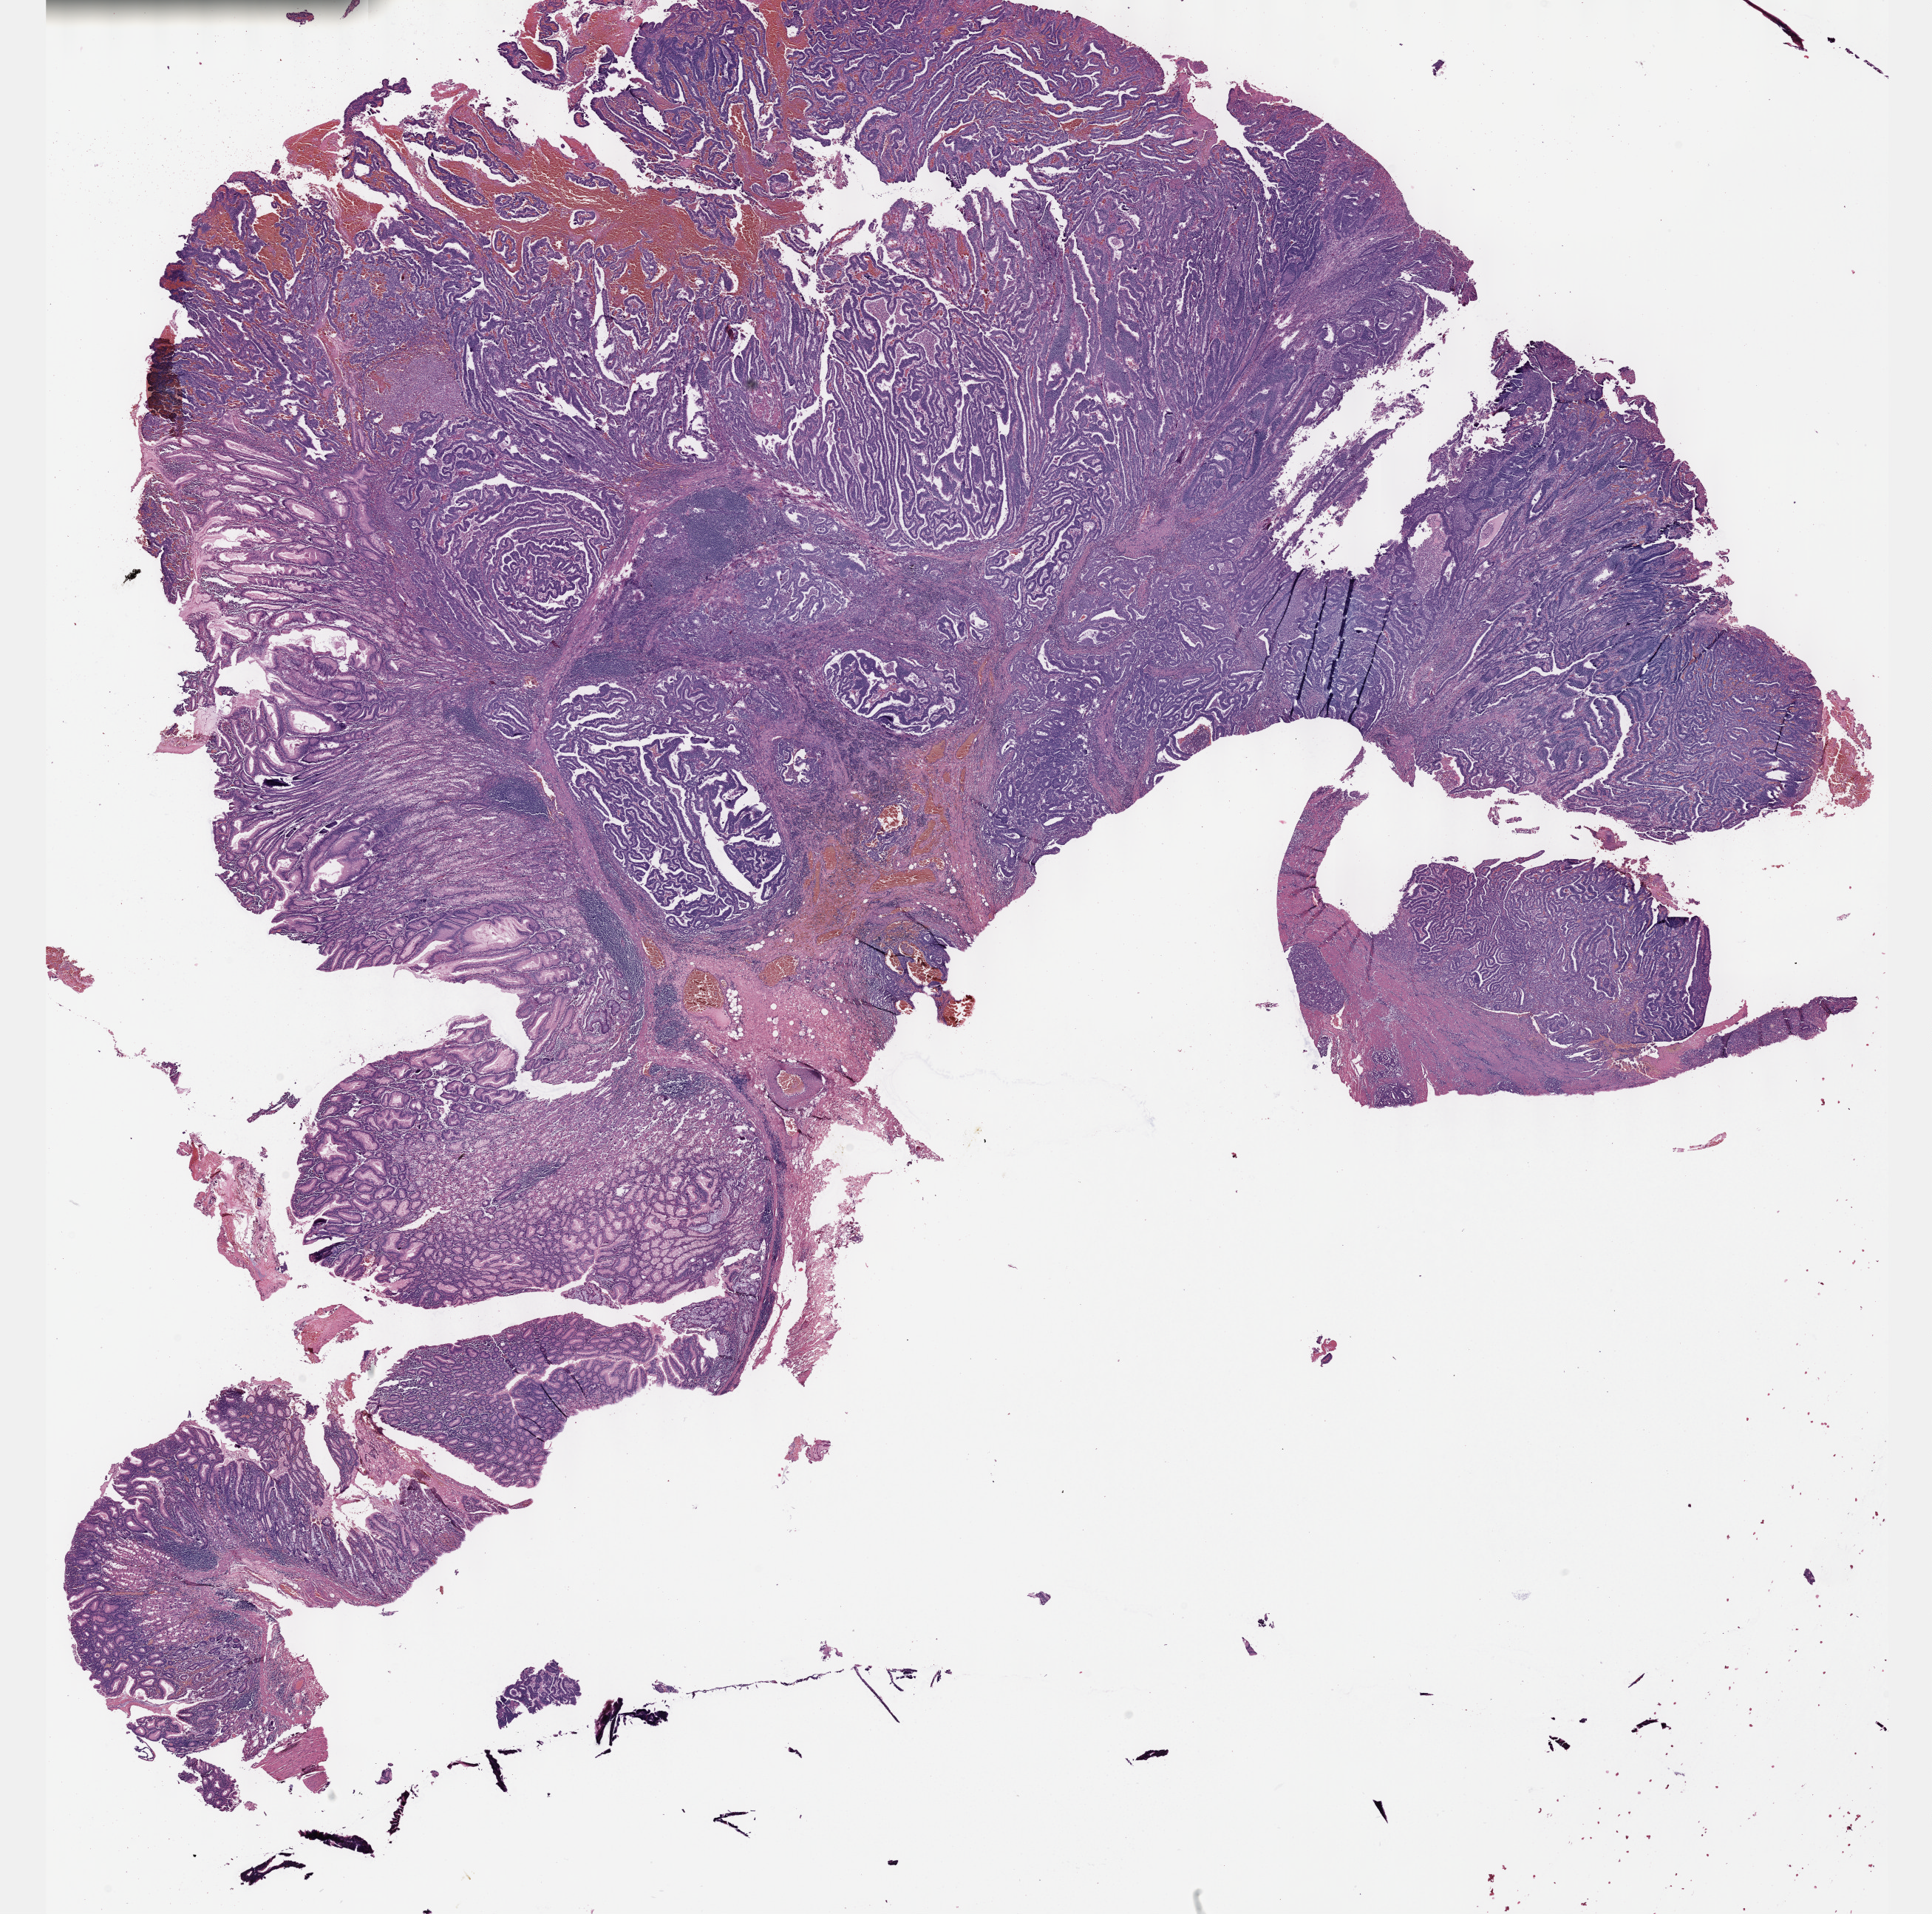
Whole-slide histology image, Hematoxylin and eosin (H&E) stained — a low-resolution overview of the entire scanned area, about 21.1 x 20.9 mm (from a 40x scan); formalin-fixed paraffin-embedded (FFPE) diagnostic section; sample: primary tumour, stomach. Male, age 30 years at initial diagnosis. Histologic grade: G2 (moderately differentiated).
AJCC pathologic stage: IIIA (6th edition). Diagnosis: Adenocarcinoma, intestinal type (body of stomach). Lymph nodes positive (case pathology): 5 of 25 examined.